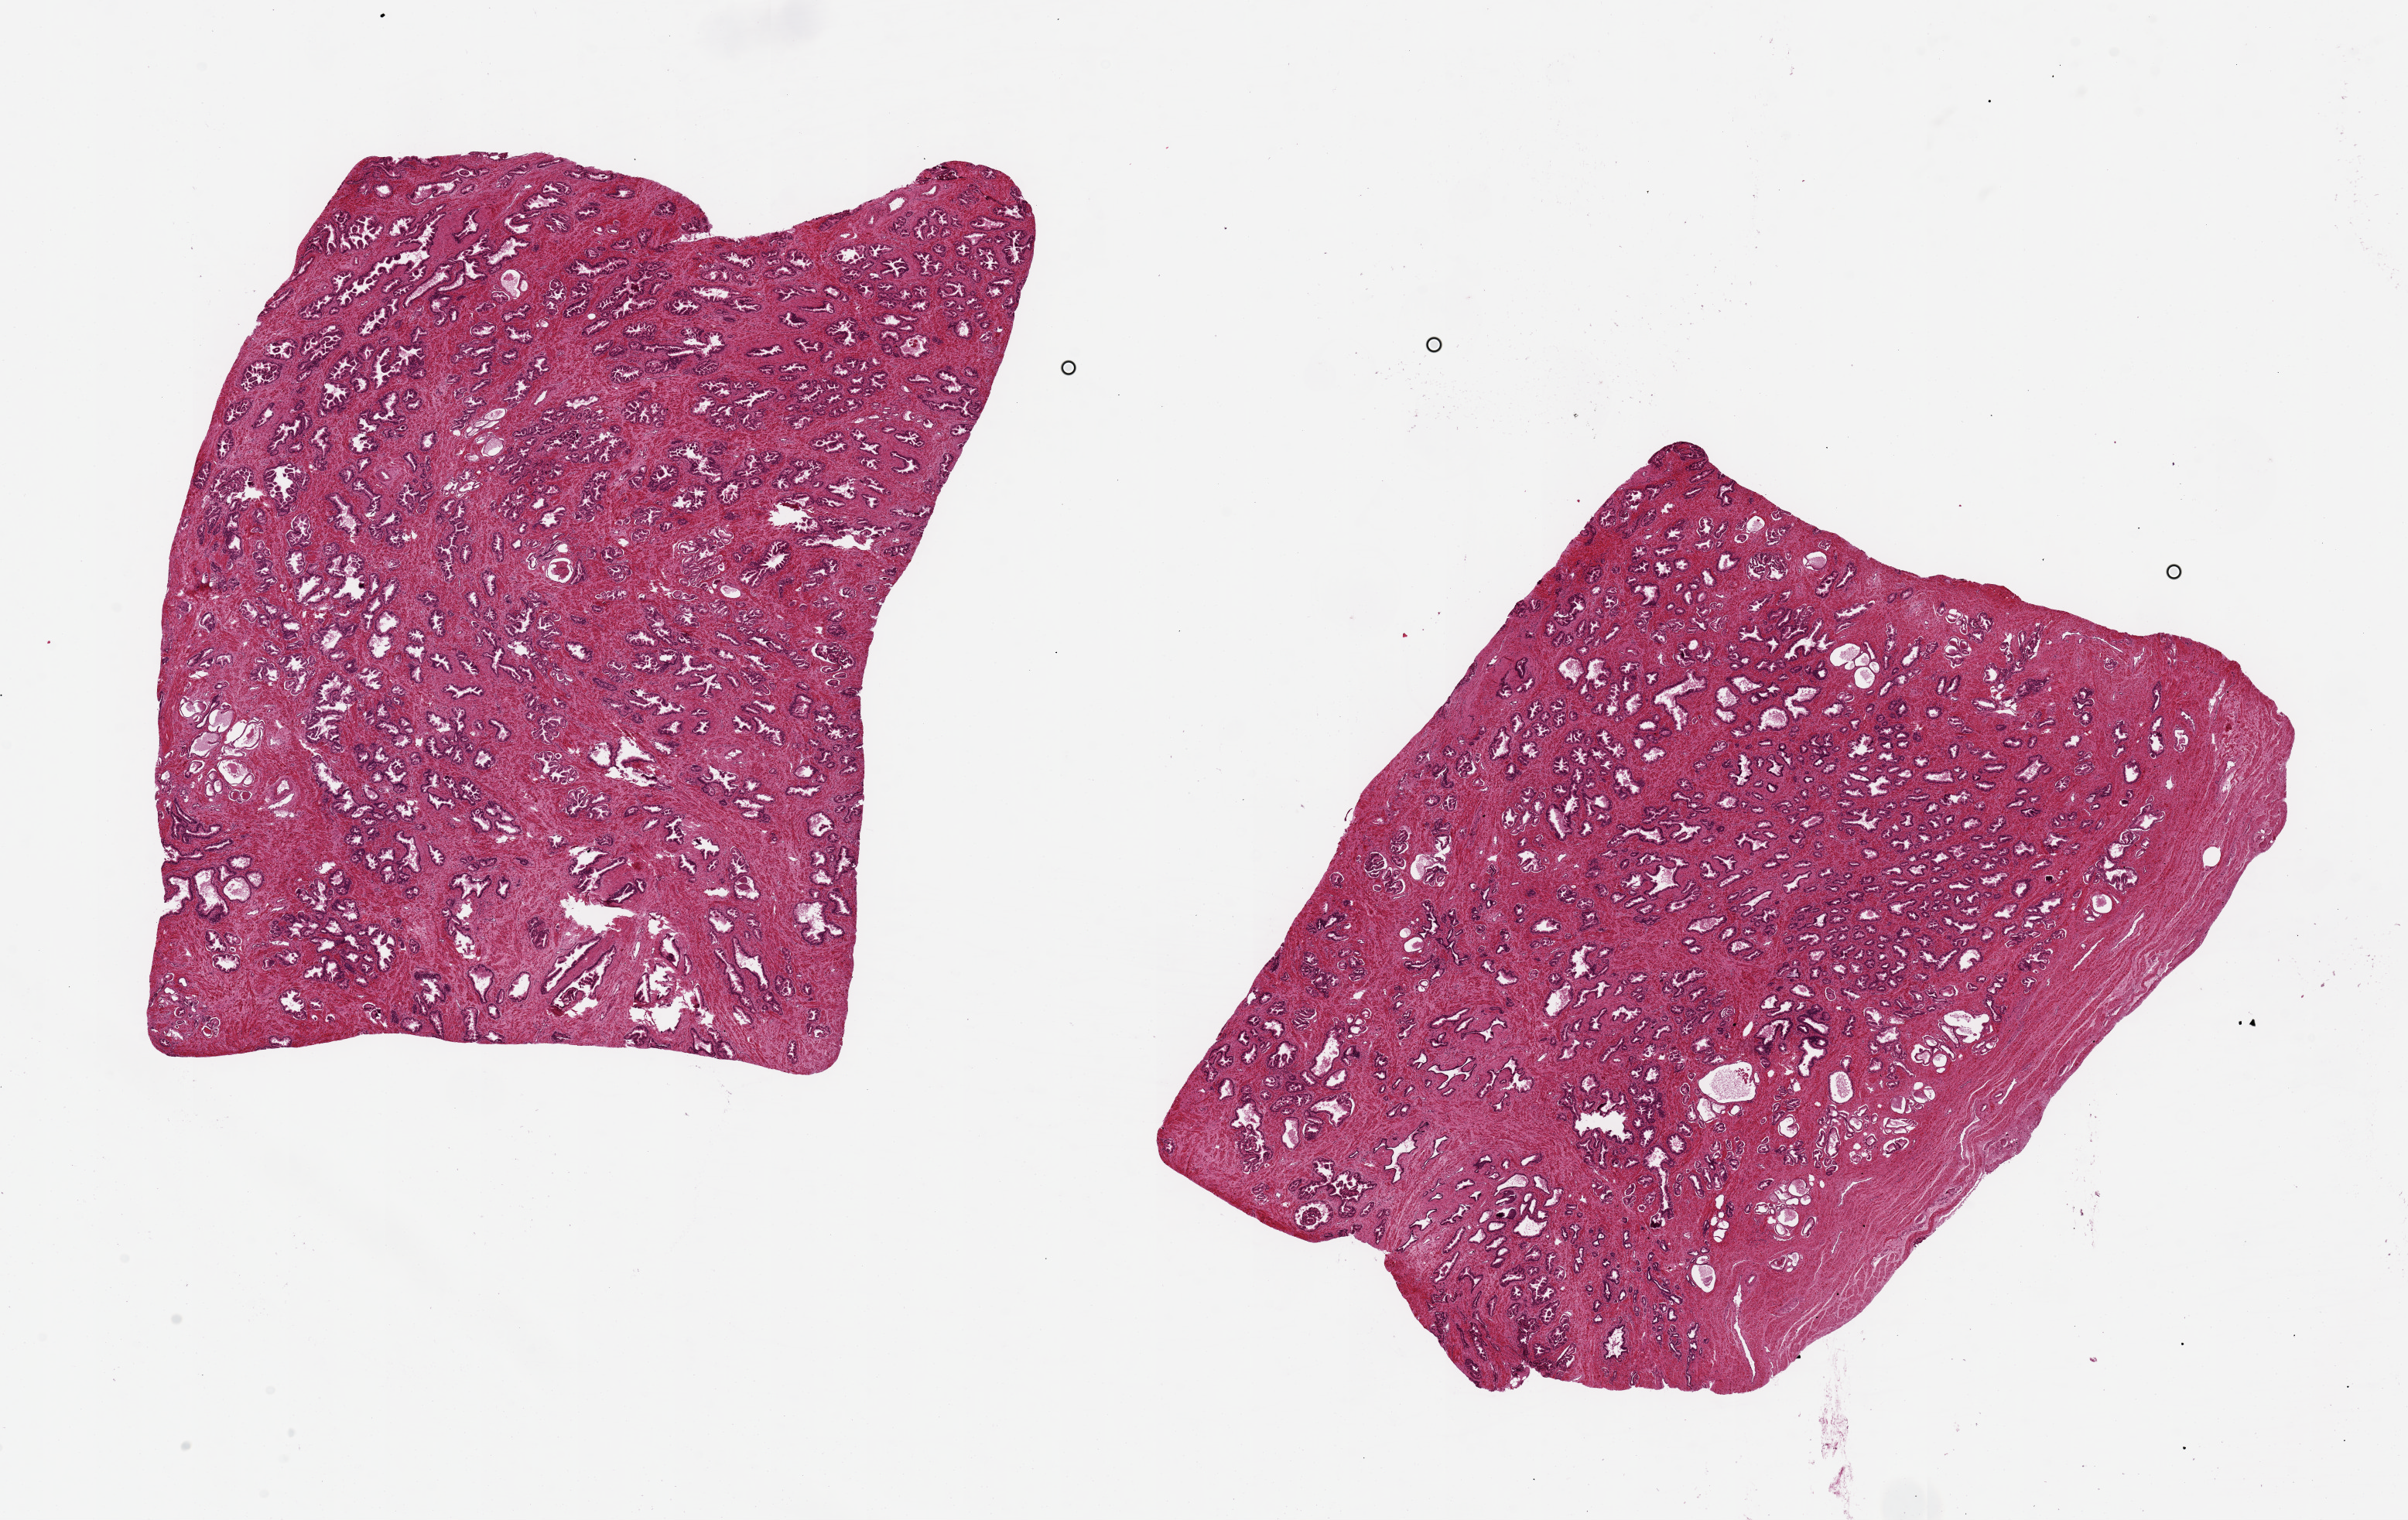
Whole-slide image, hematoxylin and eosin (H&E) stain, brightfield — shown as a low-resolution overview of the whole scanned area (about 24.6 x 15.5 mm). PAXgene-fixed paraffin-embedded (PFPE) section. Section of prostate (target tissue). Donor tissue sample. Male donor.
Review note (as recorded): 2 pieces, 7x9.5 & 9.3x8 mm; no hyperplasia.